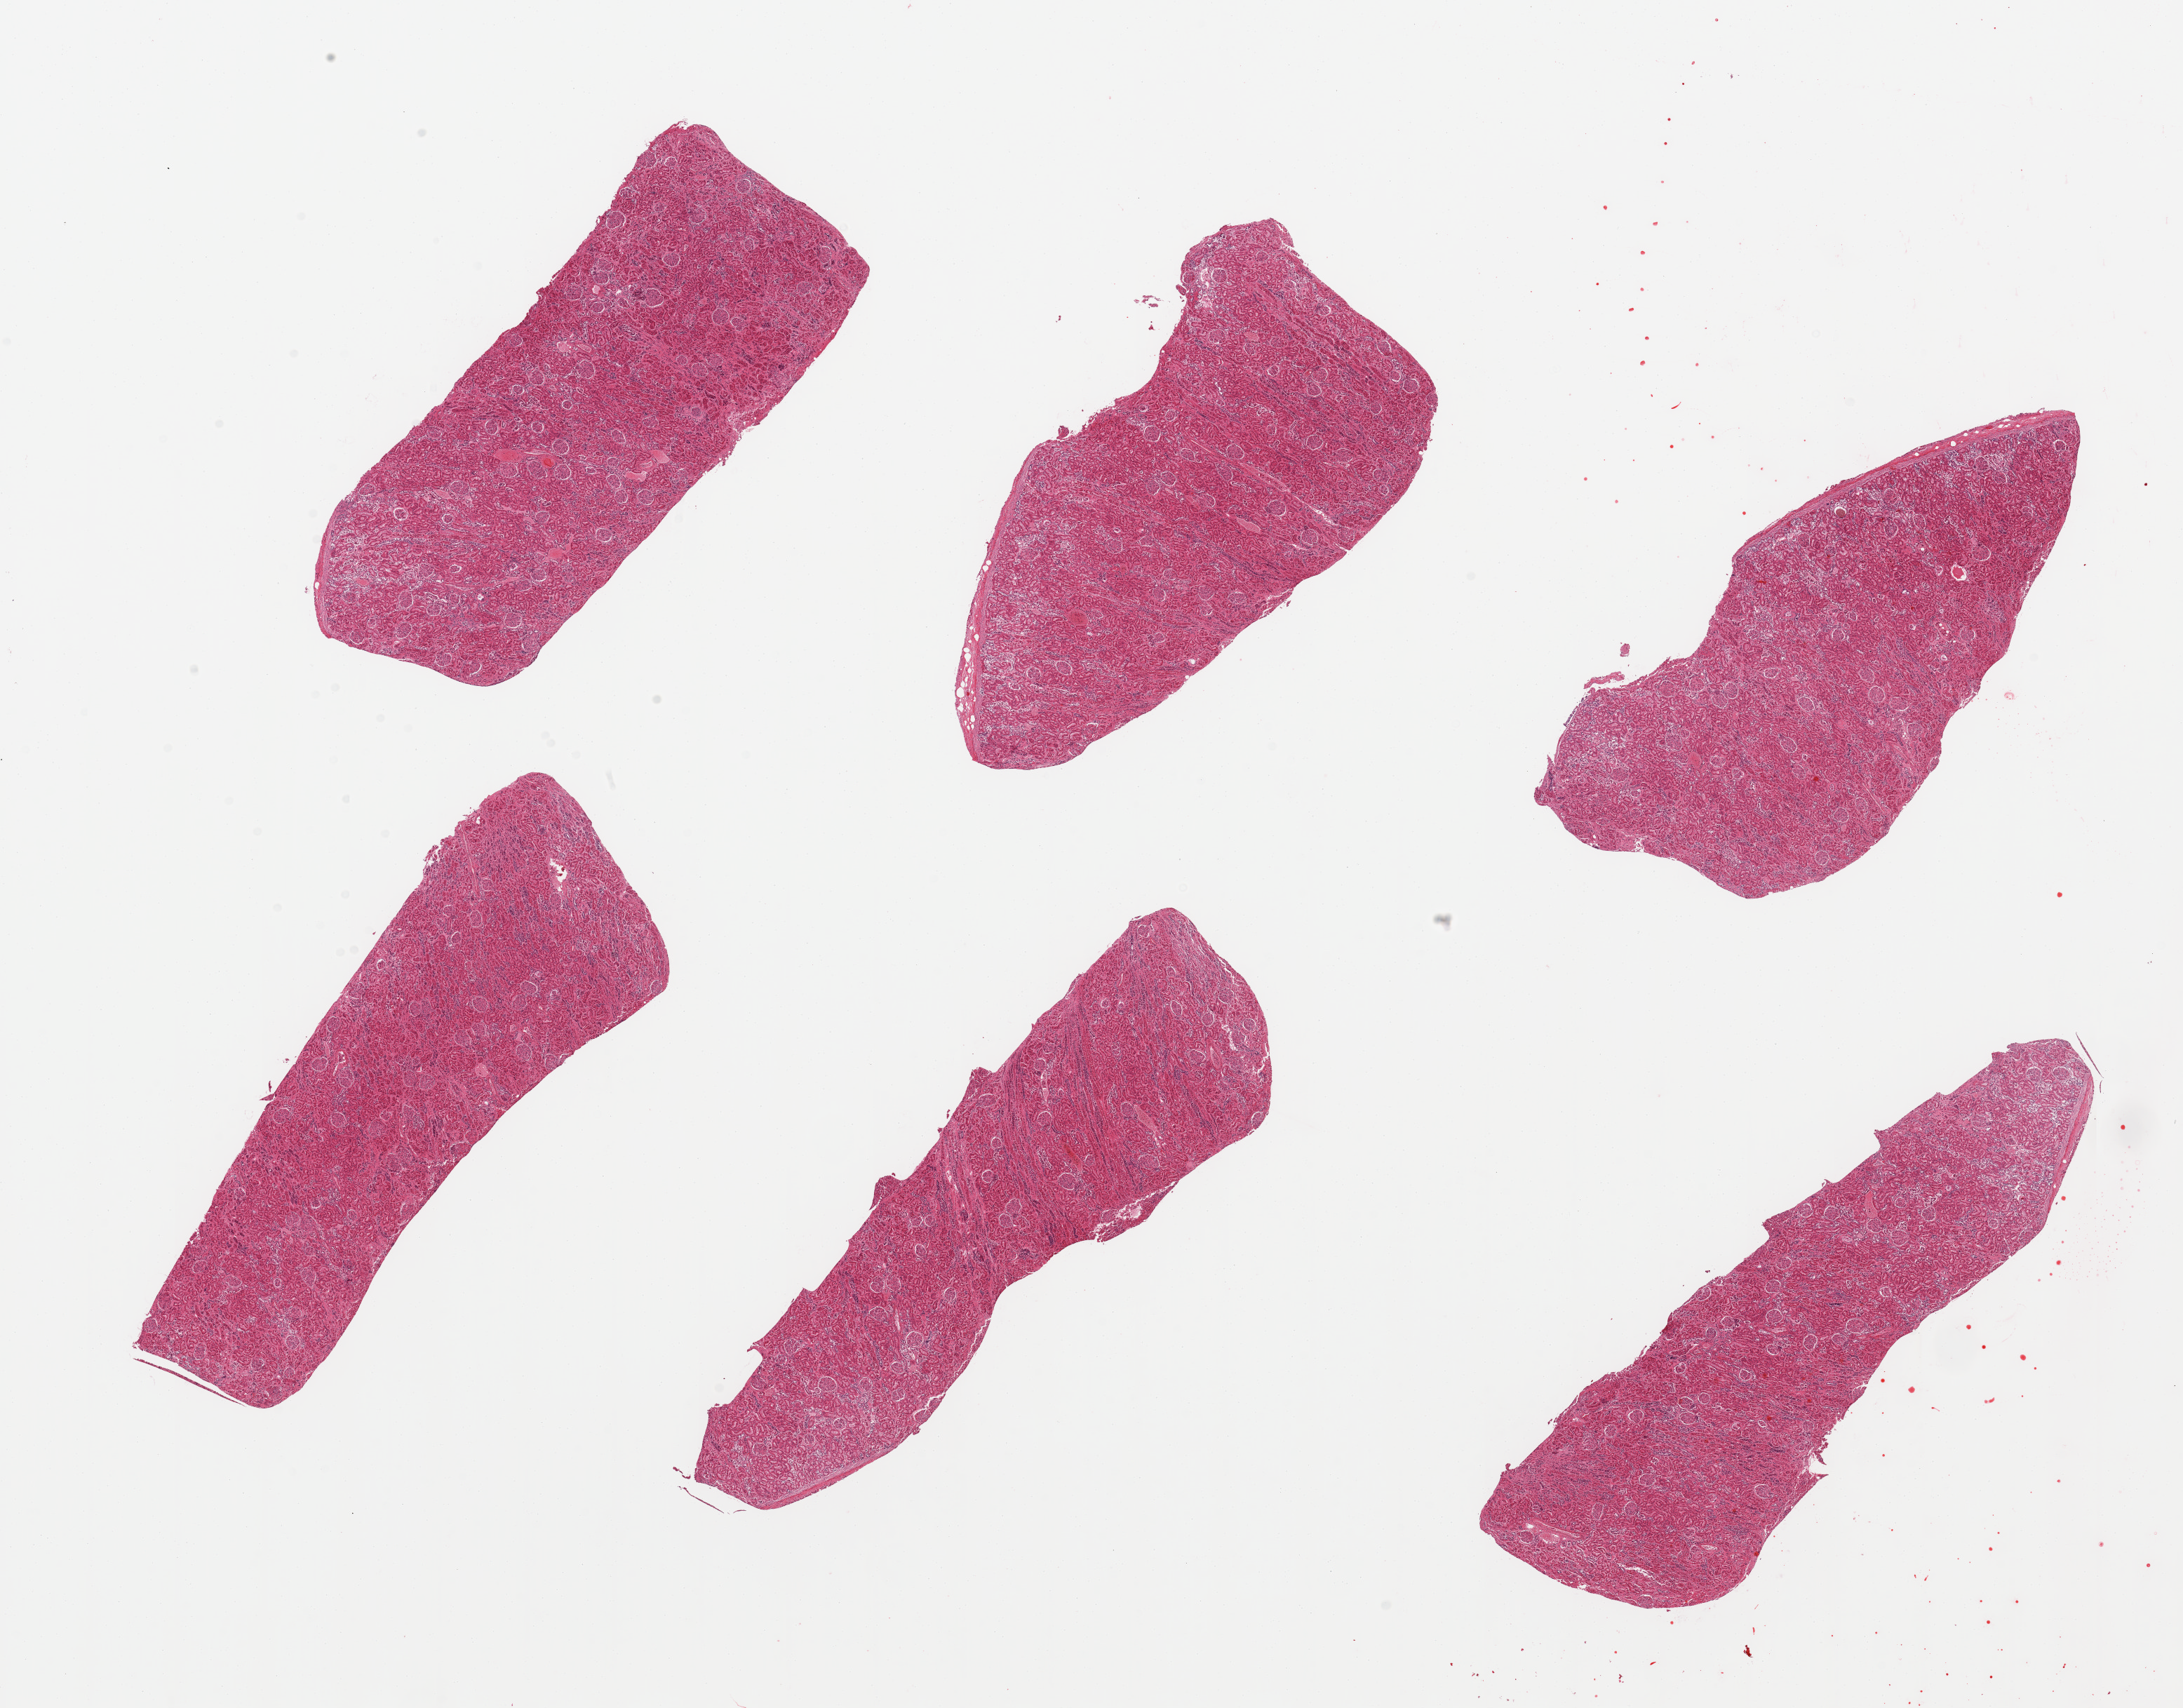
Whole-slide image, H&E stain, brightfield — shown as a low-resolution overview of the whole scanned area (about 24.6 x 19.3 mm), PAXgene-fixed paraffin-embedded (PFPE) section, target tissue: renal cortex, tissue donor sample. Donor sex: male.
Review note (as recorded): 6 pieces, glomeruli present; tubules fairly well preserved.